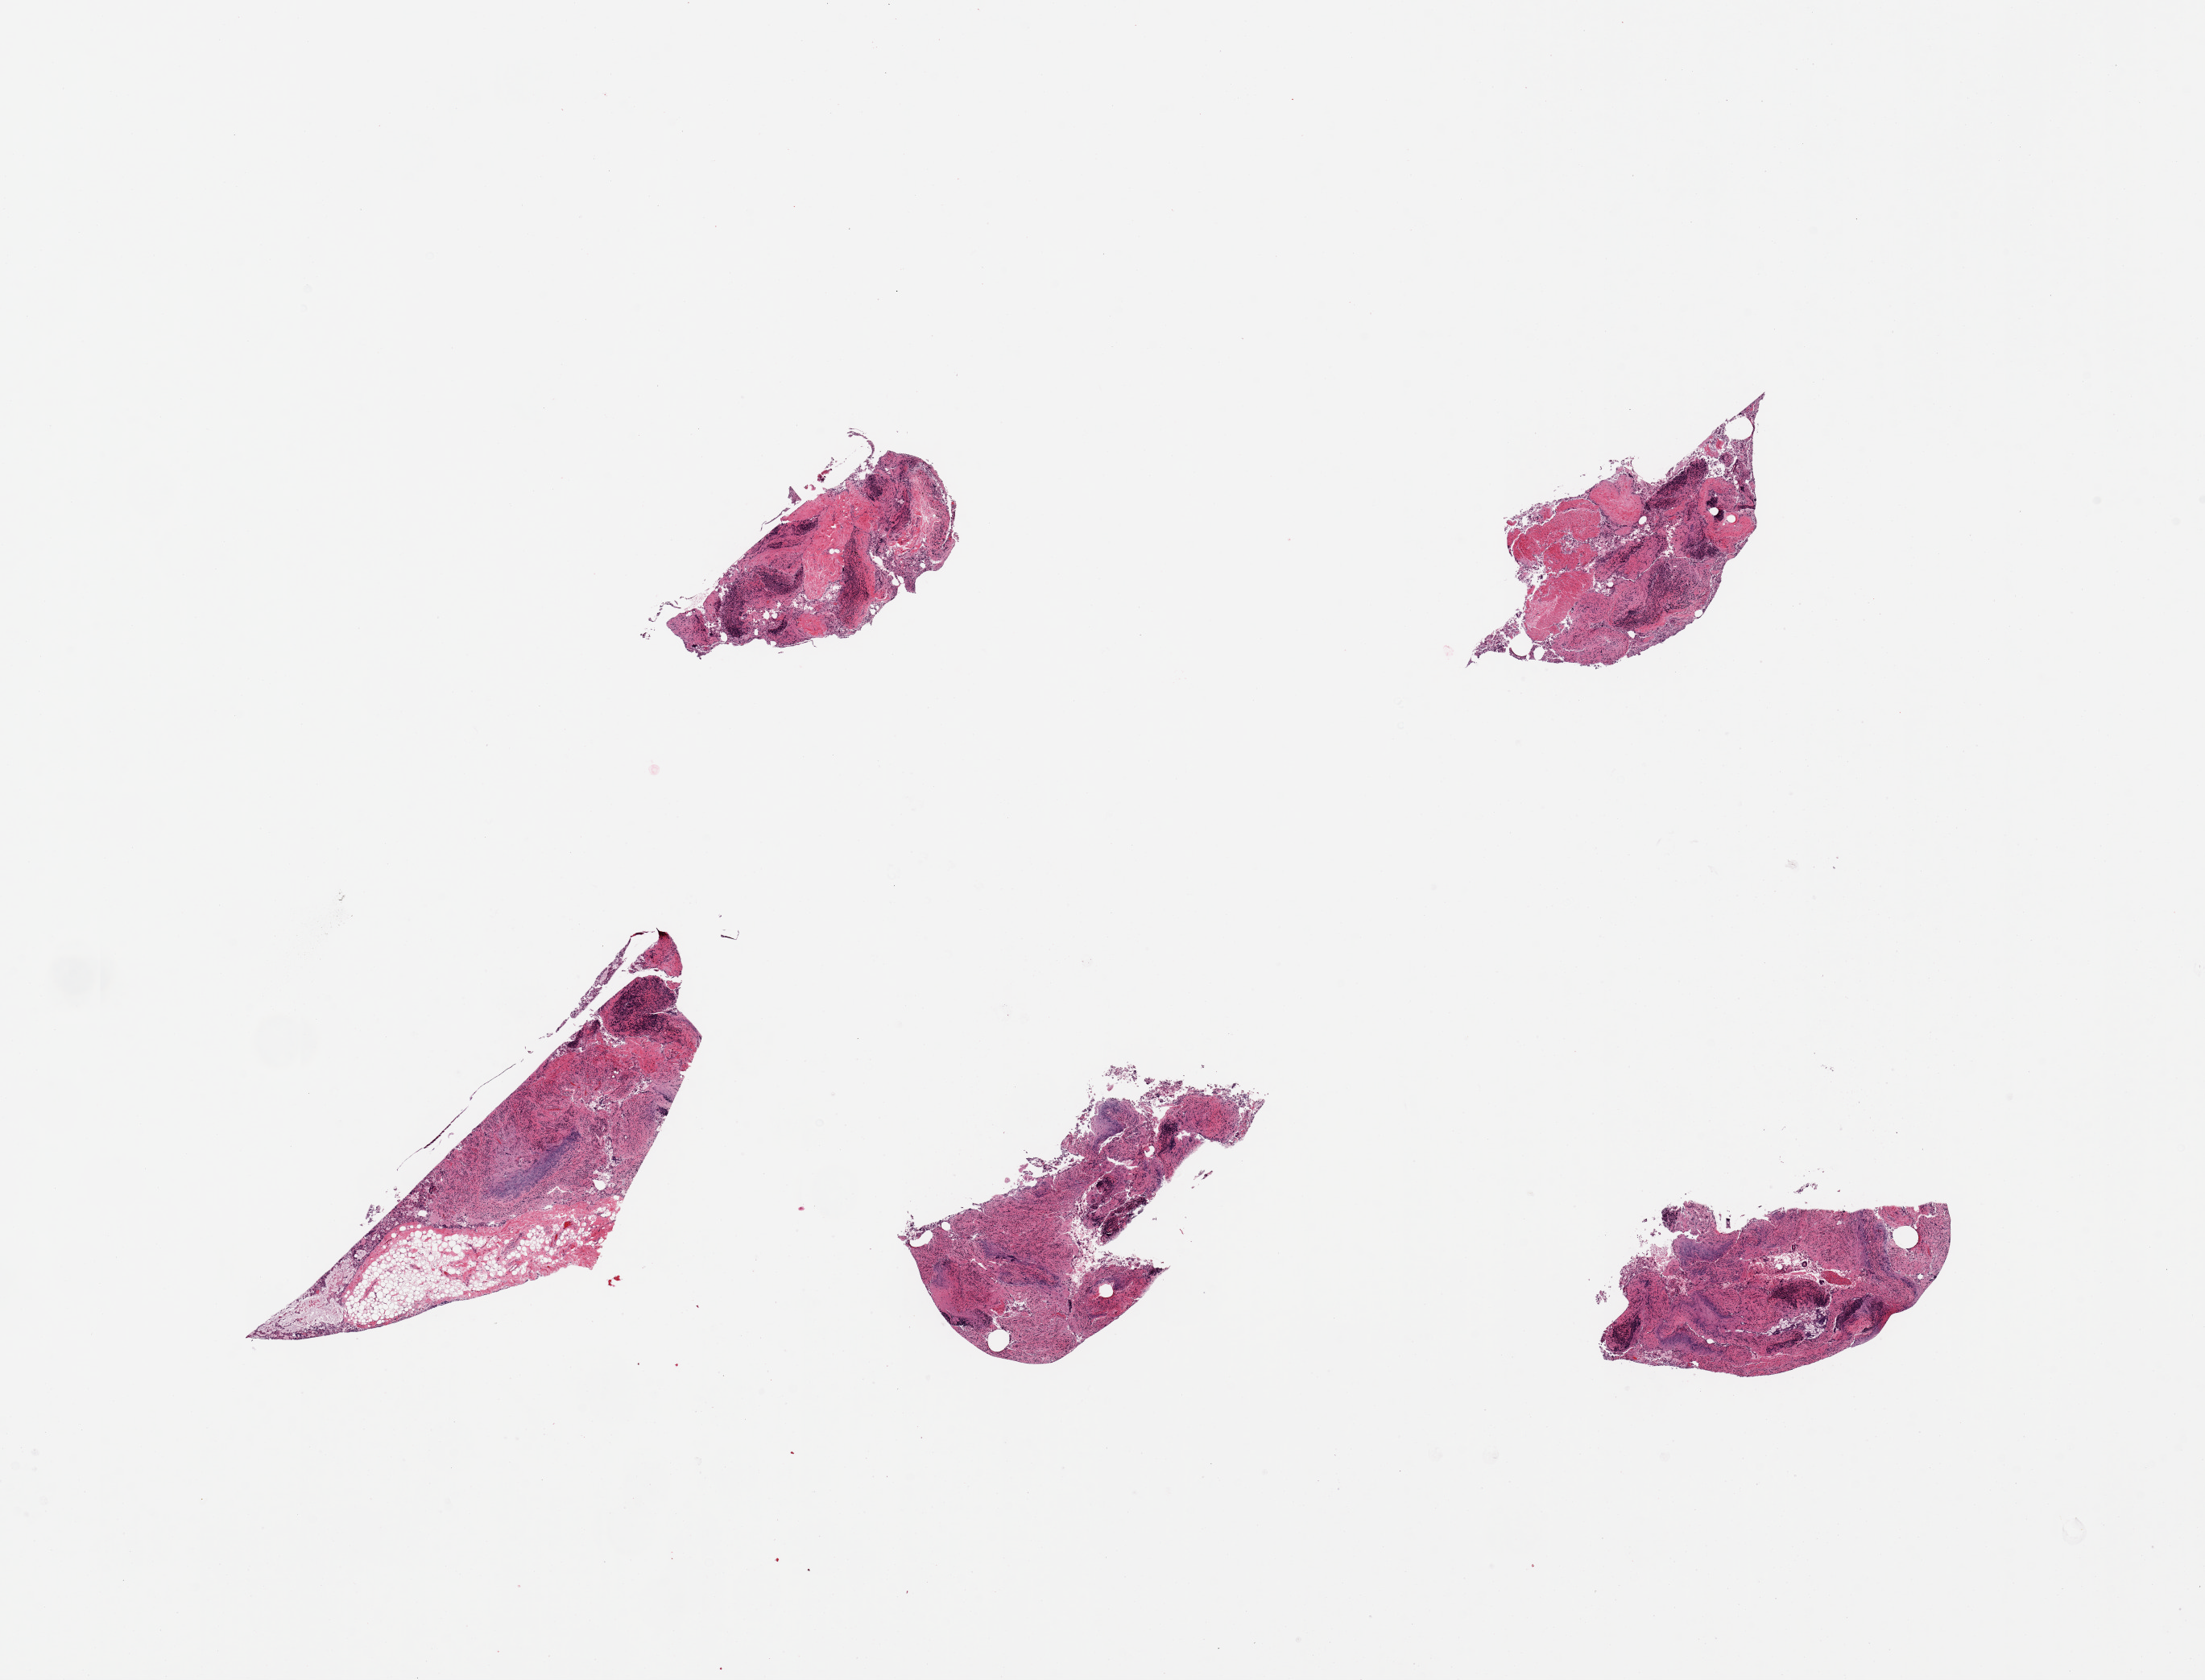
Whole-slide image, hematoxylin and eosin (H&E) stain, whole scanned area (about 21.7 x 16.5 mm) shown as a low-resolution overview, PAXgene-fixed, paraffin-embedded tissue, target tissue: ileum, tissue donor sample. Donor sex: male.
Pathologist's review note for this sample: 6 pieces; too little lymphoid tissue.